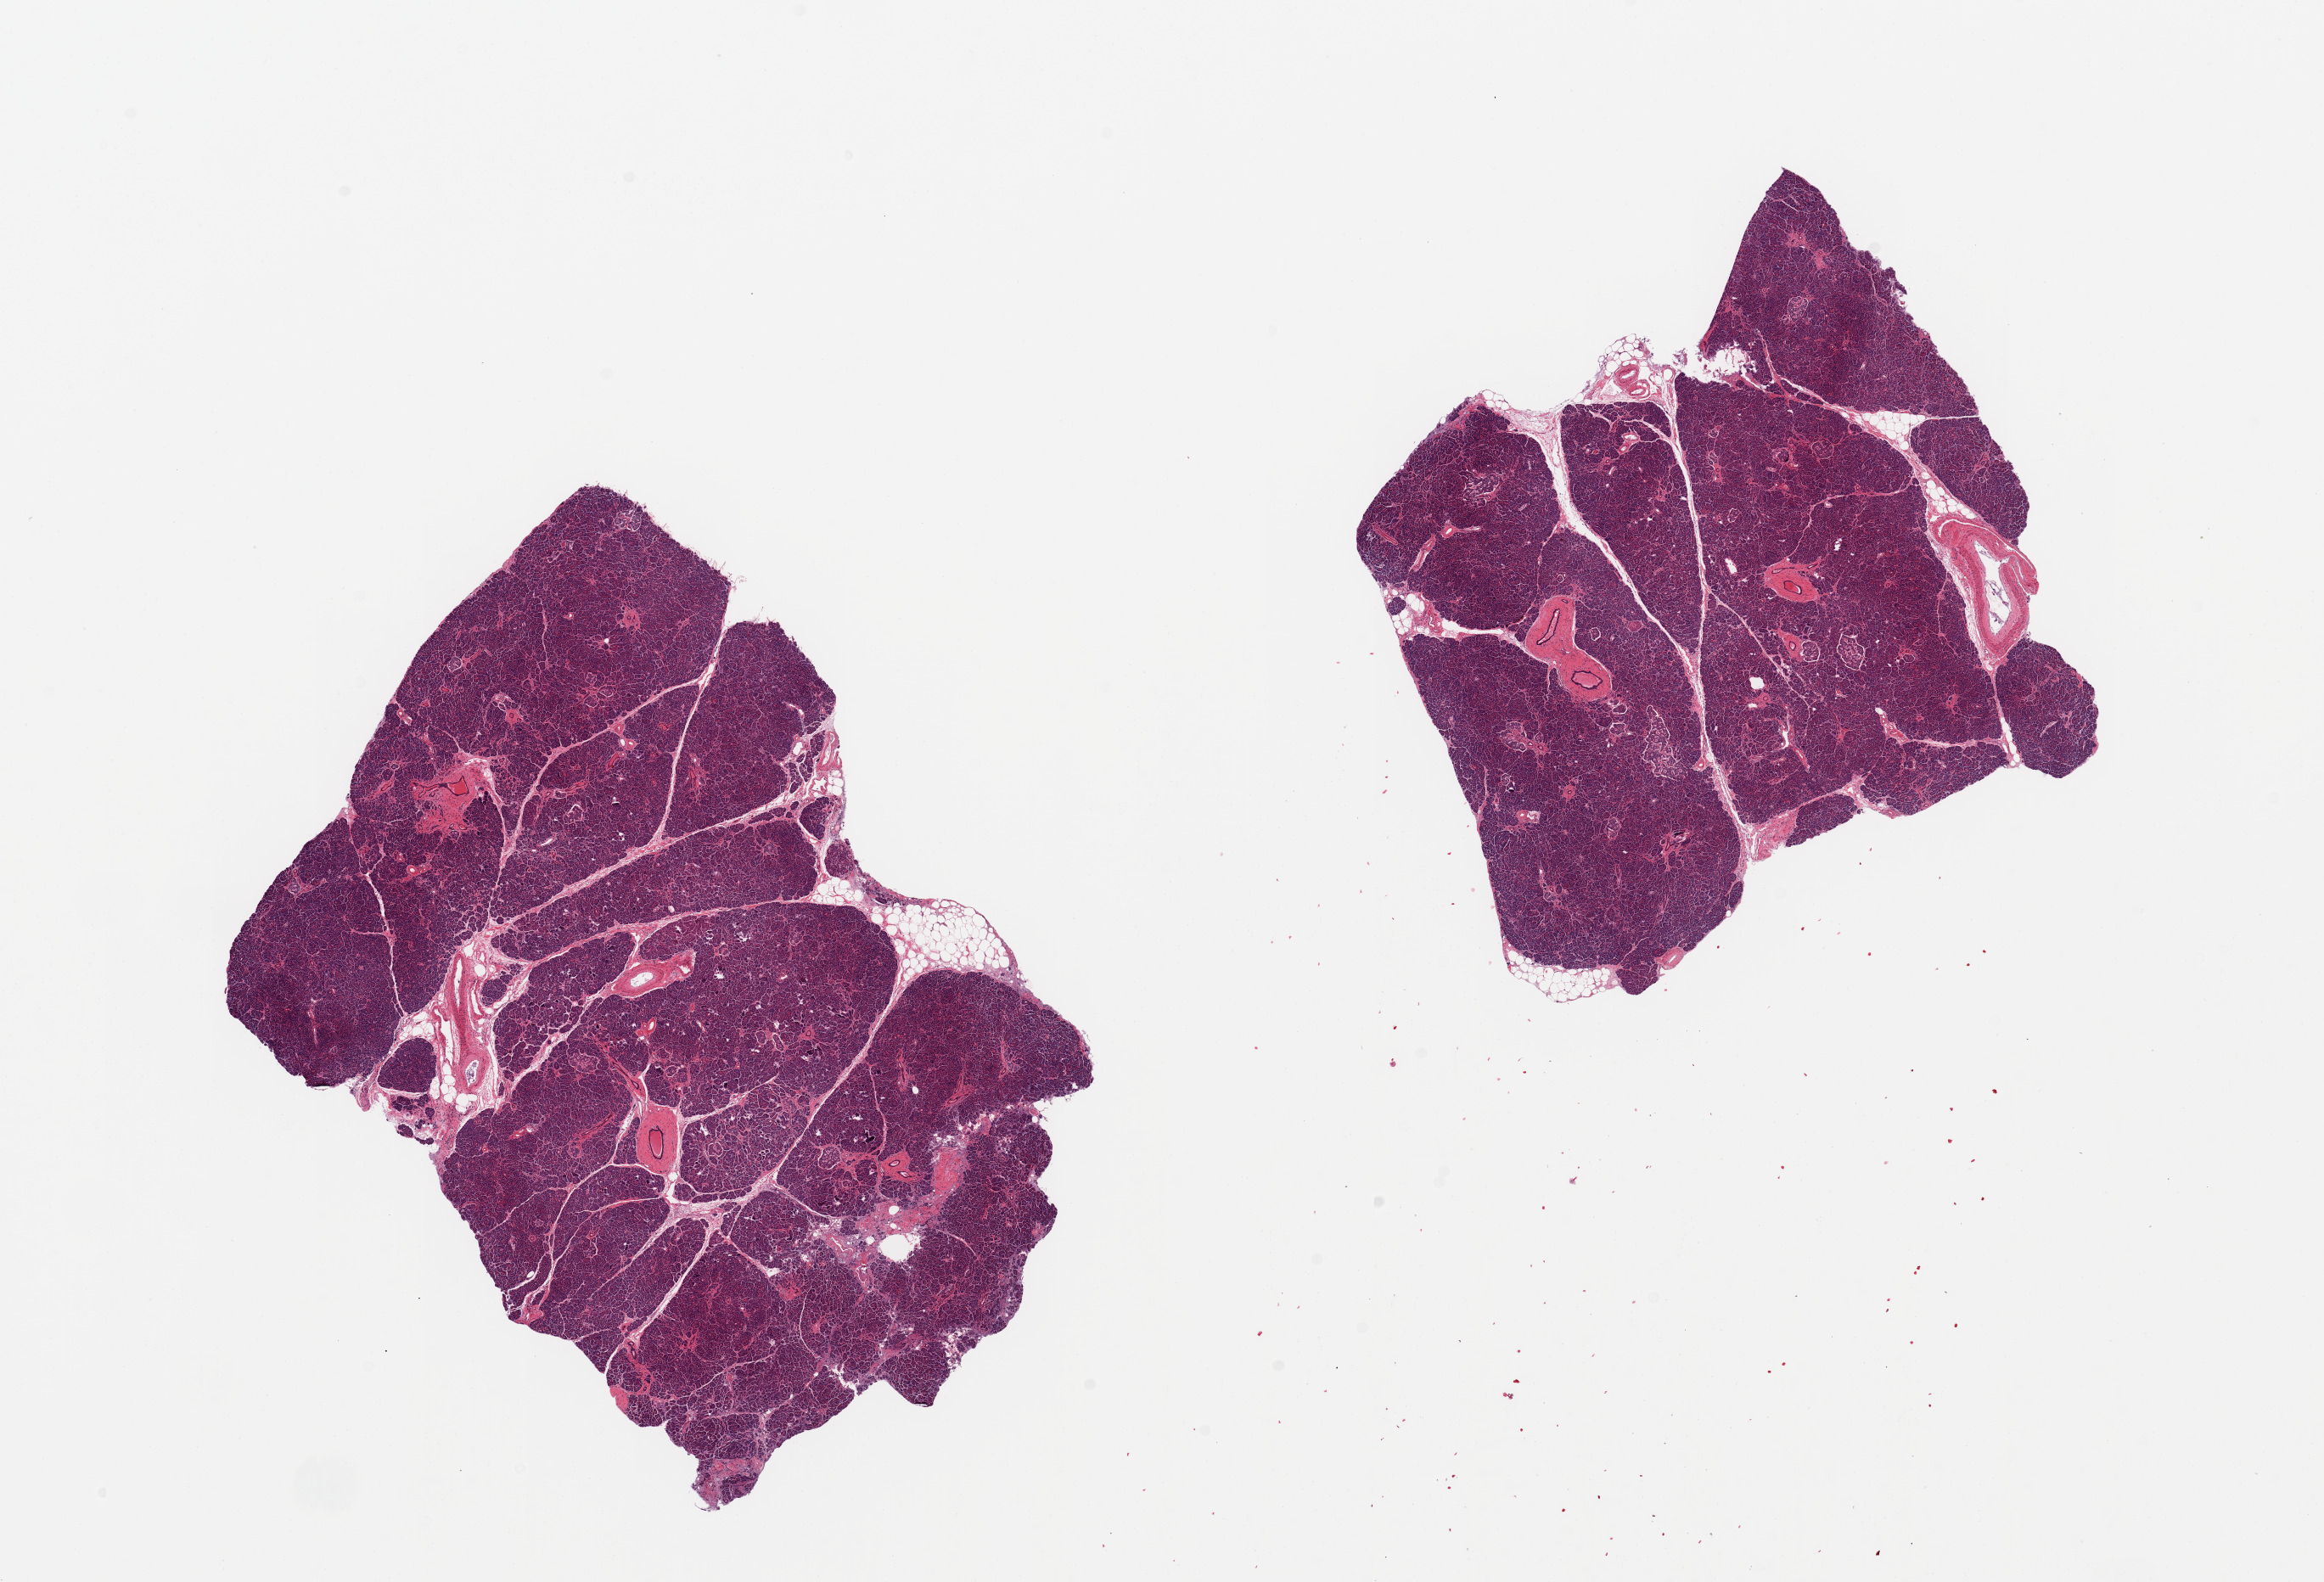
H&E whole-slide image, low-resolution overview of the scanned area, about 21.7 x 14.7 mm, PAXgene-fixed paraffin-embedded (PFPE) section, sampled site (target tissue): pancreas, tissue donor sample. Donor sex: male.
Pathologist's review note for this sample: 2 pieces; well preserved with numerous islets; <10% internal fat.